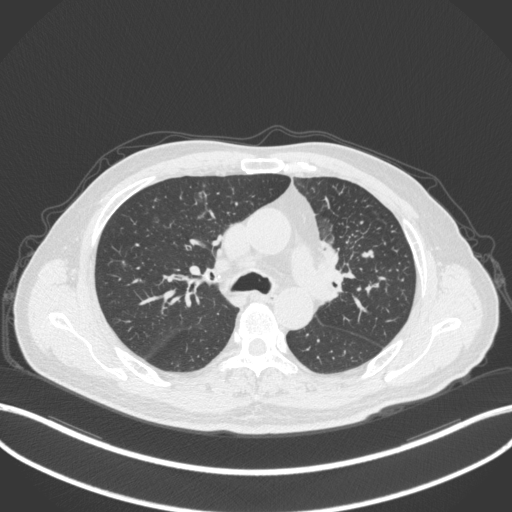
Chest CT, one axial slice; slice 226 of 386 in the series (ordered by position); 120 kVp; lung window (W 1500 / L -600 HU); 512 × 512 image matrix, field of view 400 × 400 mm. Male patient, age 69 years. From the clinical record (not read from this slice): clinical TNM (as recorded): T2a N2 M0; histopathological grade: G2-3.
Outlined on this slice (rectangle marked by the reading radiologist):
- lung tumour (recorded histology: adenocarcinoma): bounding box [x1, y1, x2, y2] px = [322, 246, 354, 293]